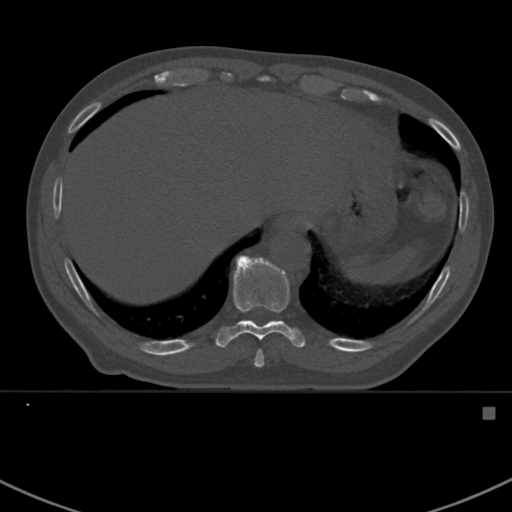
CT including the spine, one axial slice. Position 366 of 412 along the scan axis. Reconstruction kernel Br40s. 120 kVp. Bone window (W 1800 / L 400 HU). 1.5 mm slice thickness. 512 × 512 image matrix. Male patient, age 59 years. From the clinical record (not read from this slice): primary cancer: prostate.
Annotated regions visible in this slice (semi-automatically segmented with operator editing):
- T10 vertebra: box from (x=215, y=255) to (x=305, y=368) px
- T9 vertebra: (x=255, y=350)–(x=263, y=364)